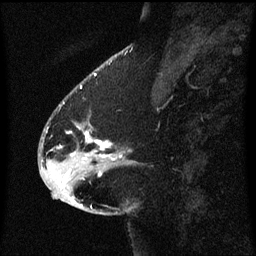
Breast MRI (dynamic contrast-enhanced), one sagittal slice; position 22 of 60 along the scan axis; dynamic contrast-enhanced series, image 2 of 3 at this slice position (ordered by acquisition); 1.5 T; TE 4.2 ms, TR 8.4 ms; 2 mm slice thickness; 256 × 256 image matrix, field of view 200 × 200 mm. Female patient, age 54 years. Case-level facts recorded for this patient, not image findings: setting: breast cancer imaged before/during neoadjuvant chemotherapy; receptor status: HR-positive, HER2-negative.
Annotated regions visible in this slice (semi-automatically segmented with operator editing):
- analysis volume of interest (the breast-tissue region the enhancement analysis was run in; not a lesion): bounding box [x1, y1, x2, y2] px = [46, 102, 123, 171]
- tumour enhancement mask (voxels above the 70 % enhancement threshold inside the analysis volume of interest): [70, 132, 112, 149]